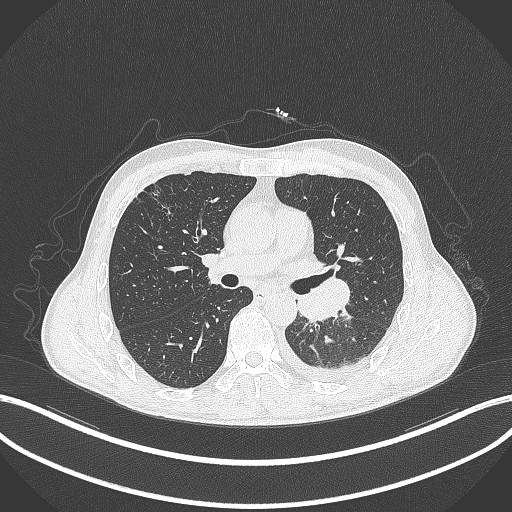
Chest CT, one axial slice; 120 kVp; lung window (W 1500 / L -600 HU); 1 mm slice thickness; 512 × 512 image matrix, field of view 400 × 400 mm. Patient: male, 47 years. Case-level facts recorded for this patient, not image findings: clinical TNM (as recorded): T3 N1 M1c; histopathological grade: G3.
Structures marked on this image (bounding box drawn by a radiologist):
- lung tumour (recorded histology: small cell carcinoma): bounding box (x1, y1, x2, y2) in pixels: (293, 275, 351, 326)